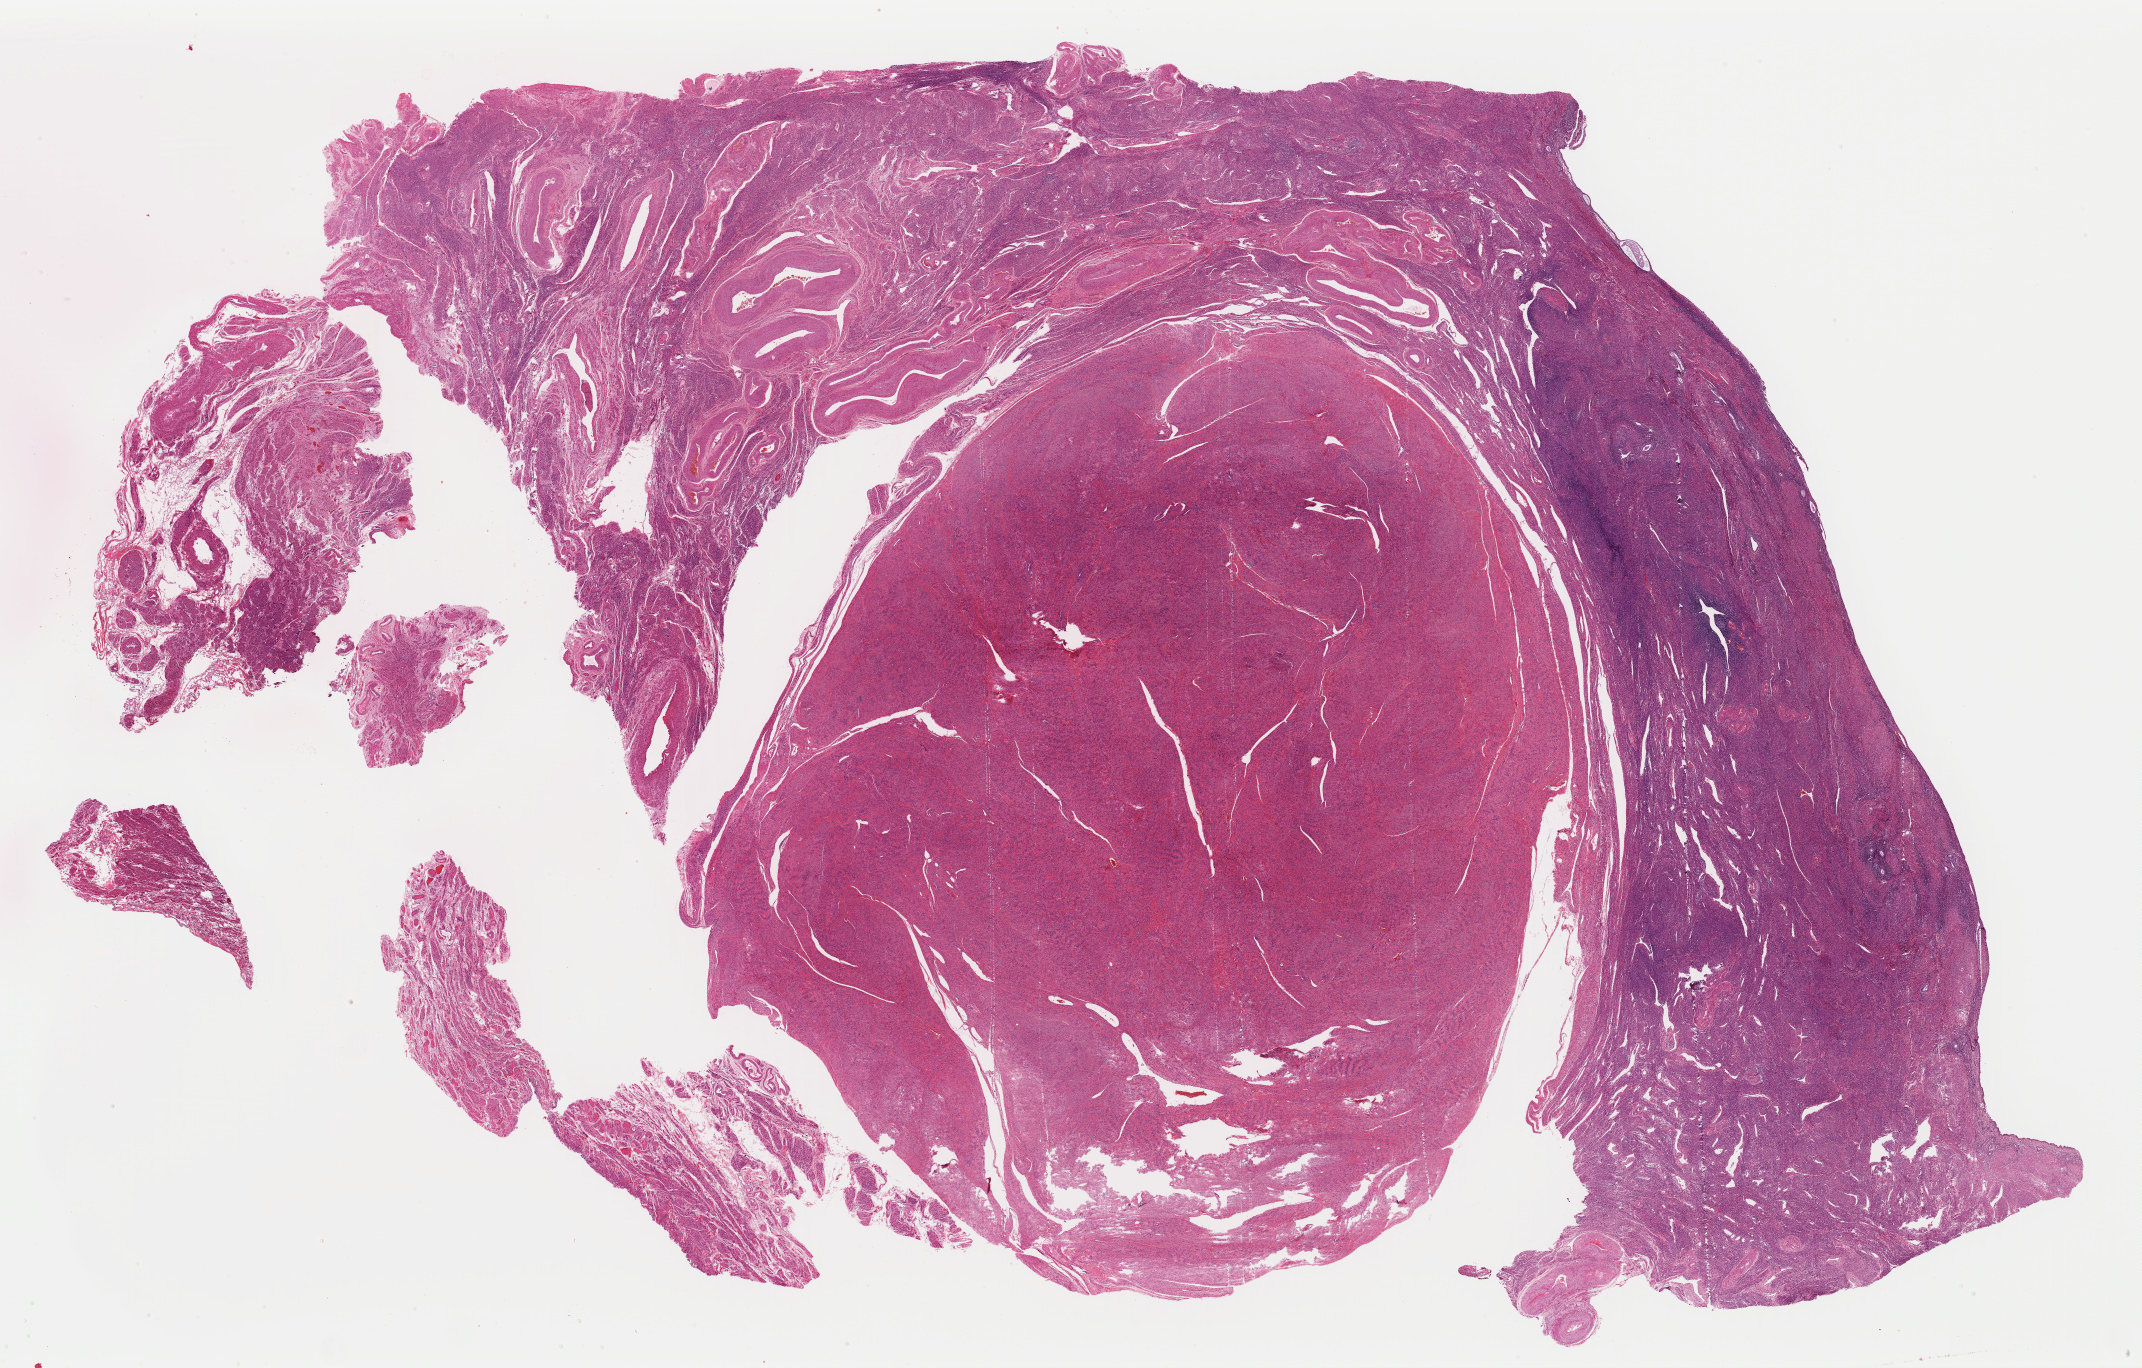
Digitized H&E tissue section (whole slide), a low-resolution overview of the entire scanned area, about 33.8 x 21.6 mm (slide scanned at 40x). FFPE section. Sample: primary tumour, uterus. Female patient; age at initial diagnosis 68 years. Histologic grade: G3 (poorly differentiated).
Pathologic diagnosis: Serous cystadenocarcinoma, NOS (endometrium). FIGO stage: IA.